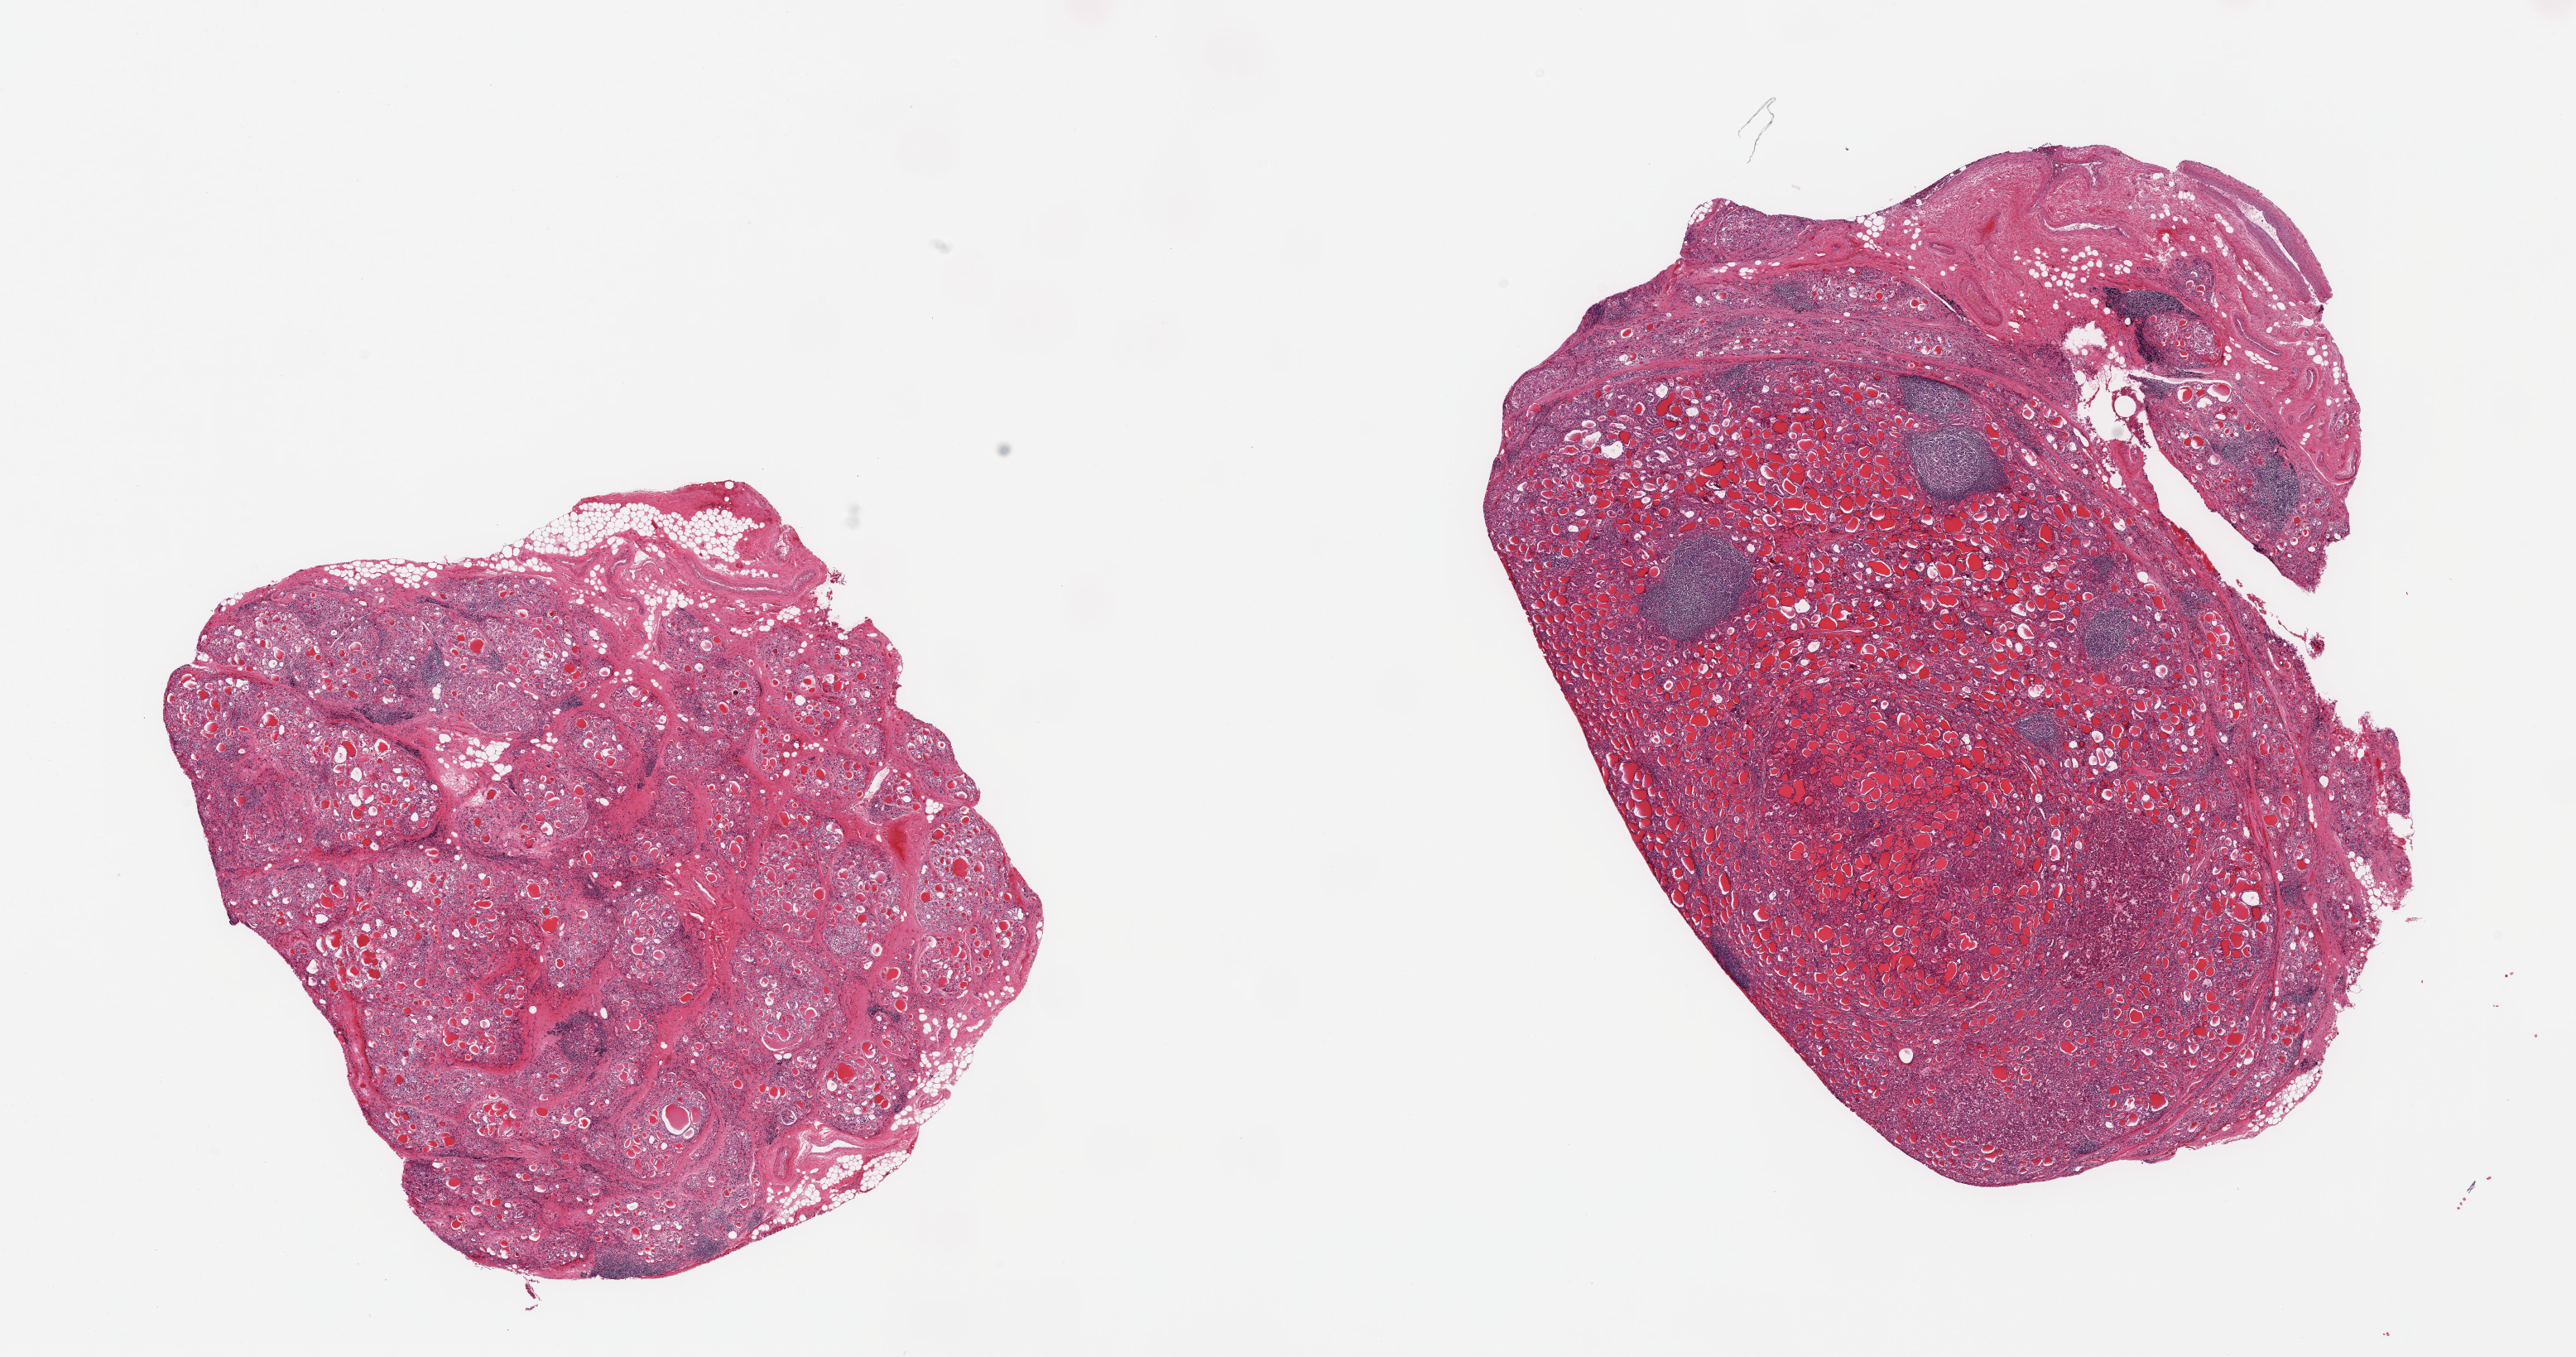
Whole-slide image, H&E stain, brightfield — low-resolution overview of the scanned area, about 24.6 x 13.0 mm; PAXgene-fixed paraffin-embedded (PFPE) section; section of thyroid (target tissue); donor tissue sample. Male donor.
Reviewer comment on this tissue sample: 2 pieces, nodulear goiter with Hashimoto thyroiditis.